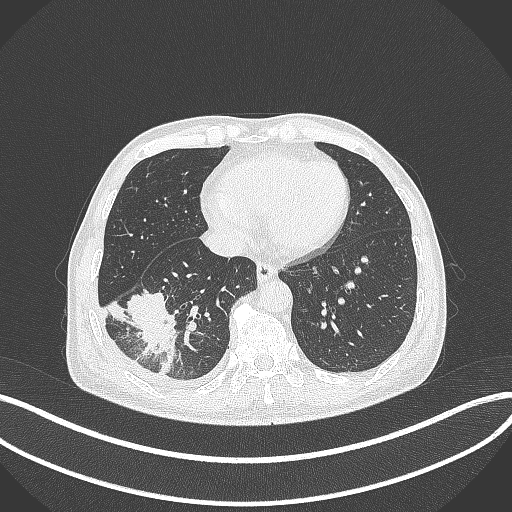
Chest CT, one axial slice; slice 119 of 388 in the series (ordered by position); 120 kVp; lung window (W 1500 / L -600 HU); 1 mm slice thickness; 512 × 512 image matrix, field of view 400 × 400 mm. Male patient, age 64 years. From the clinical record (not read from this slice): clinical TNM (as recorded): T3 N0 M0.
Outlined on this slice (bounding box drawn by a radiologist):
- lung tumour (recorded histology: adenocarcinoma): box from (x=121, y=286) to (x=182, y=379) px